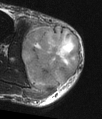
MRI of an extremity soft-tissue mass, one axial slice; position 25 of 48 along the scan axis; T2-weighted fat-saturated; MR volume resampled by the dataset authors to the PET/CT grid (not the native acquisition matrix); 3.27 mm slice thickness; 102 × 119 image matrix. Male patient. From the clinical record (not read from this slice): histological type: pleiomorphic liposarcoma; grade: high; site of the primary tumour: right calf.
Annotated regions visible in this slice (expert contour drawn on MRI and transferred to this co-registered scan by the dataset authors):
- gross tumour volume including surrounding oedema: bounding box [x1, y1, x2, y2] px = [21, 19, 81, 100]
- gross tumour volume (mass): [21, 26, 81, 86]